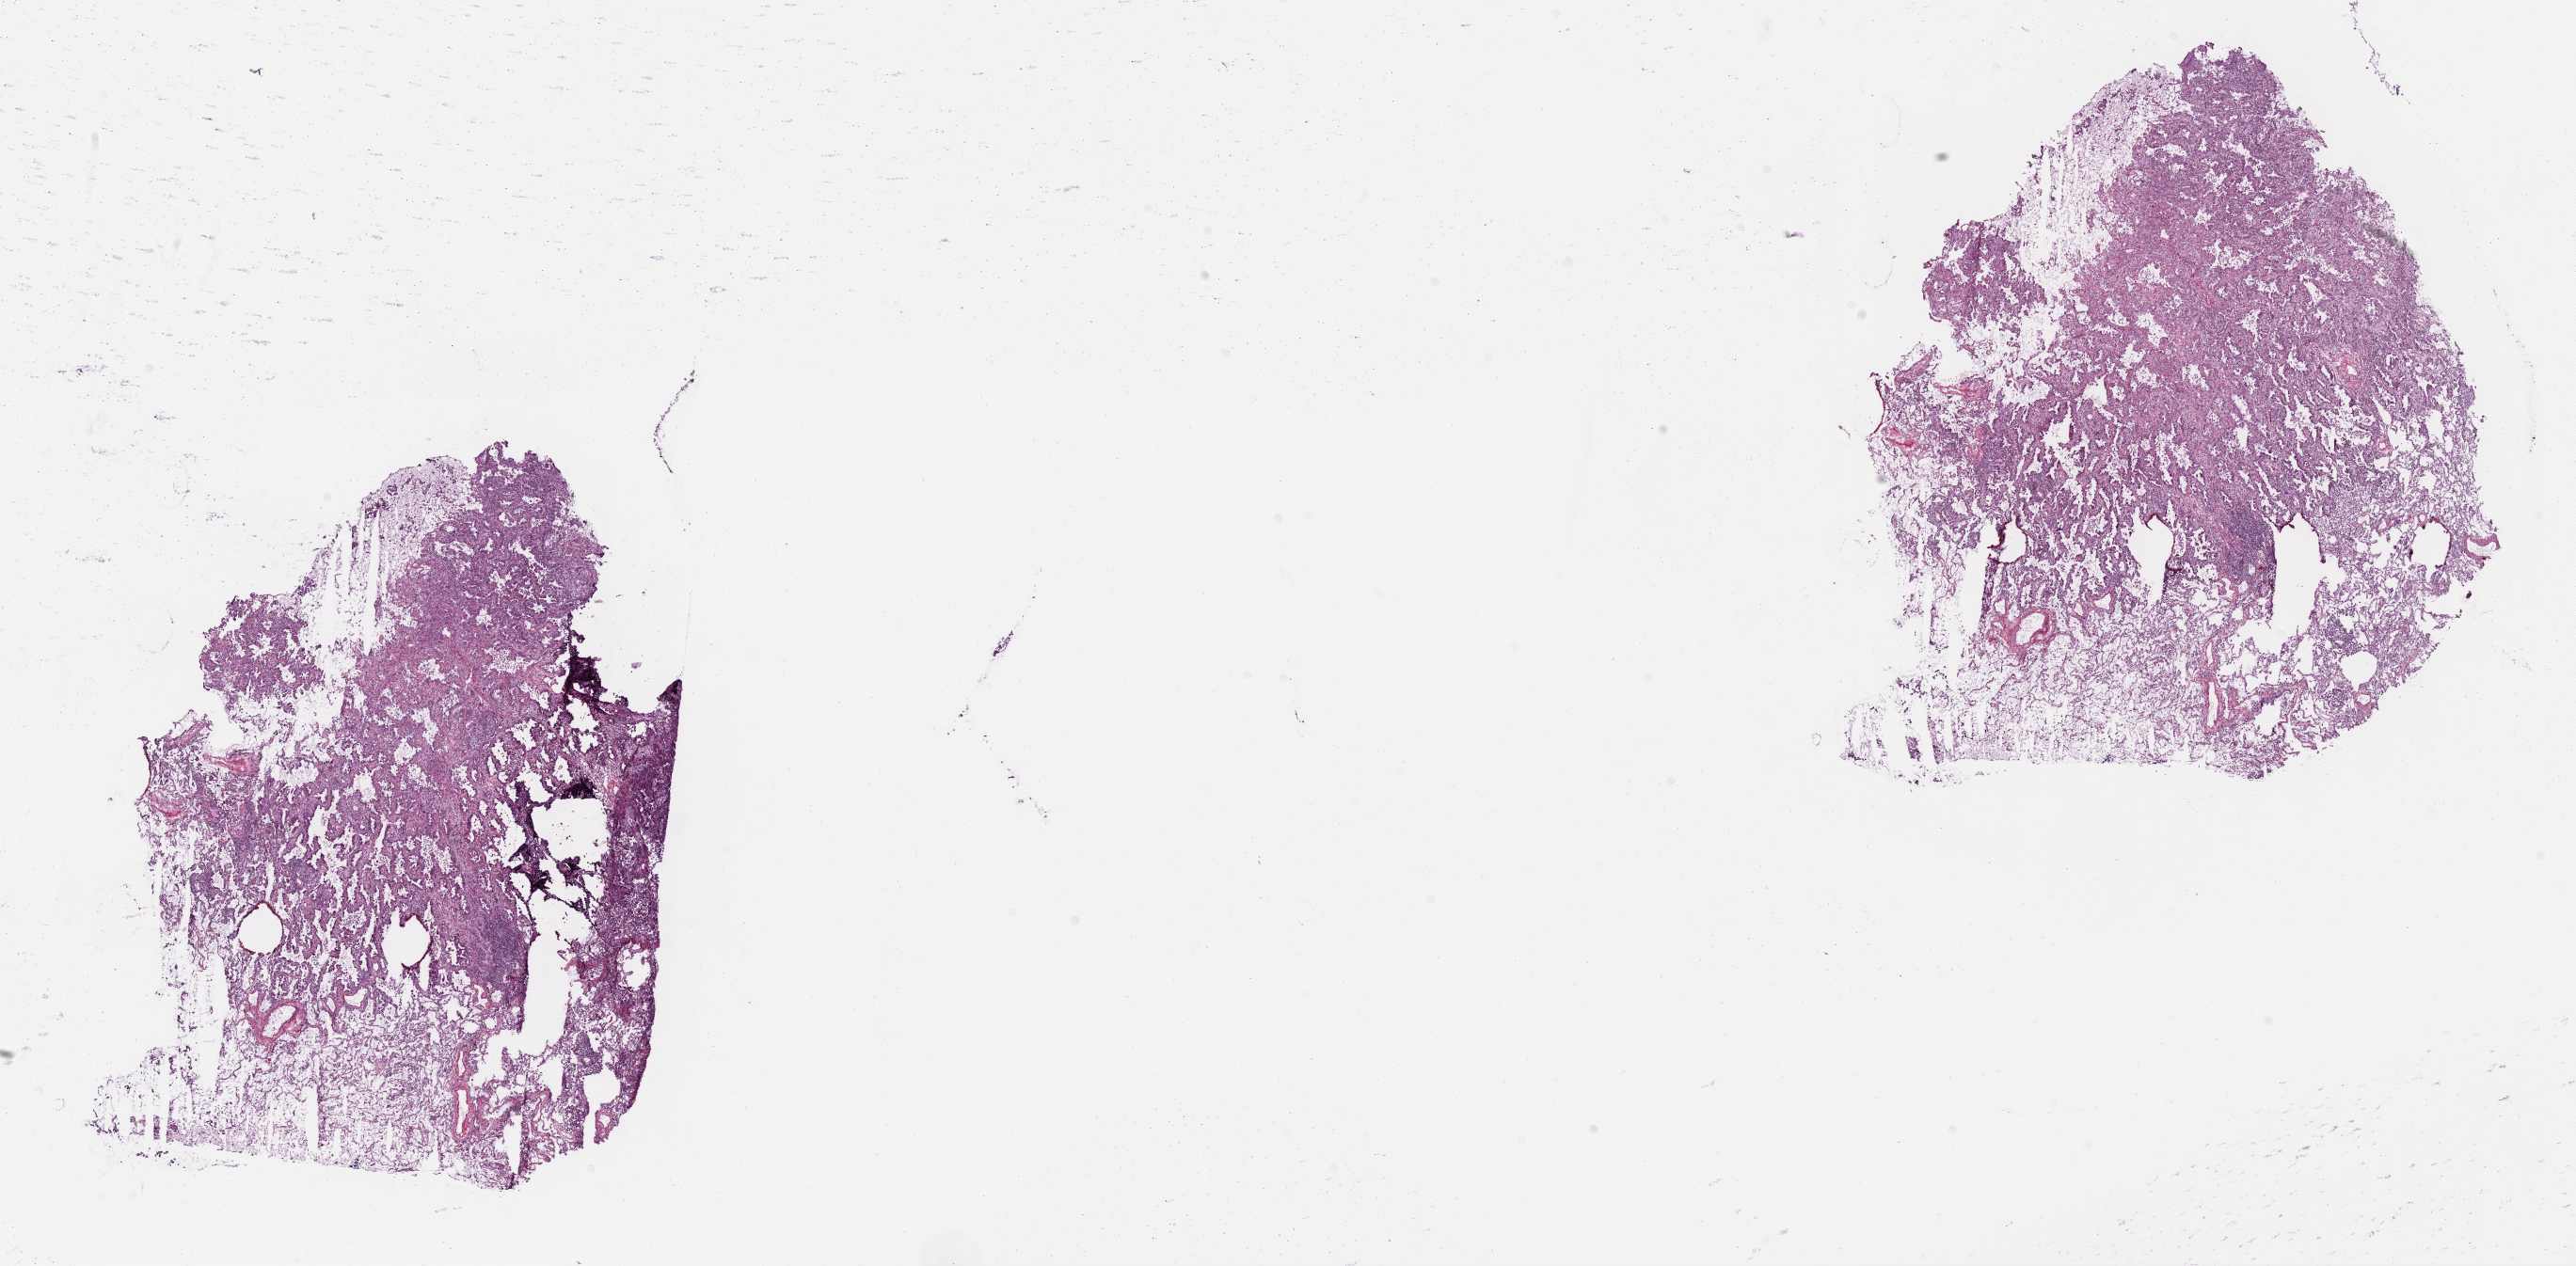
Whole-slide histology image, H&E, low-resolution overview of the scanned area, about 22.1 x 10.9 mm (acquisition: 40x scan). Frozen section. Lung, primary tumour sample. Male patient; age at initial diagnosis 72 years. Pathologist review of this section (percent, as recorded): tumour nuclei 70%, necrosis 3%.
• laterality: right
• AJCC pathologic stage: IA (7th edition)
• histologic diagnosis: Acinar cell carcinoma (upper lobe, lung)
• TNM: T1 N0 MX